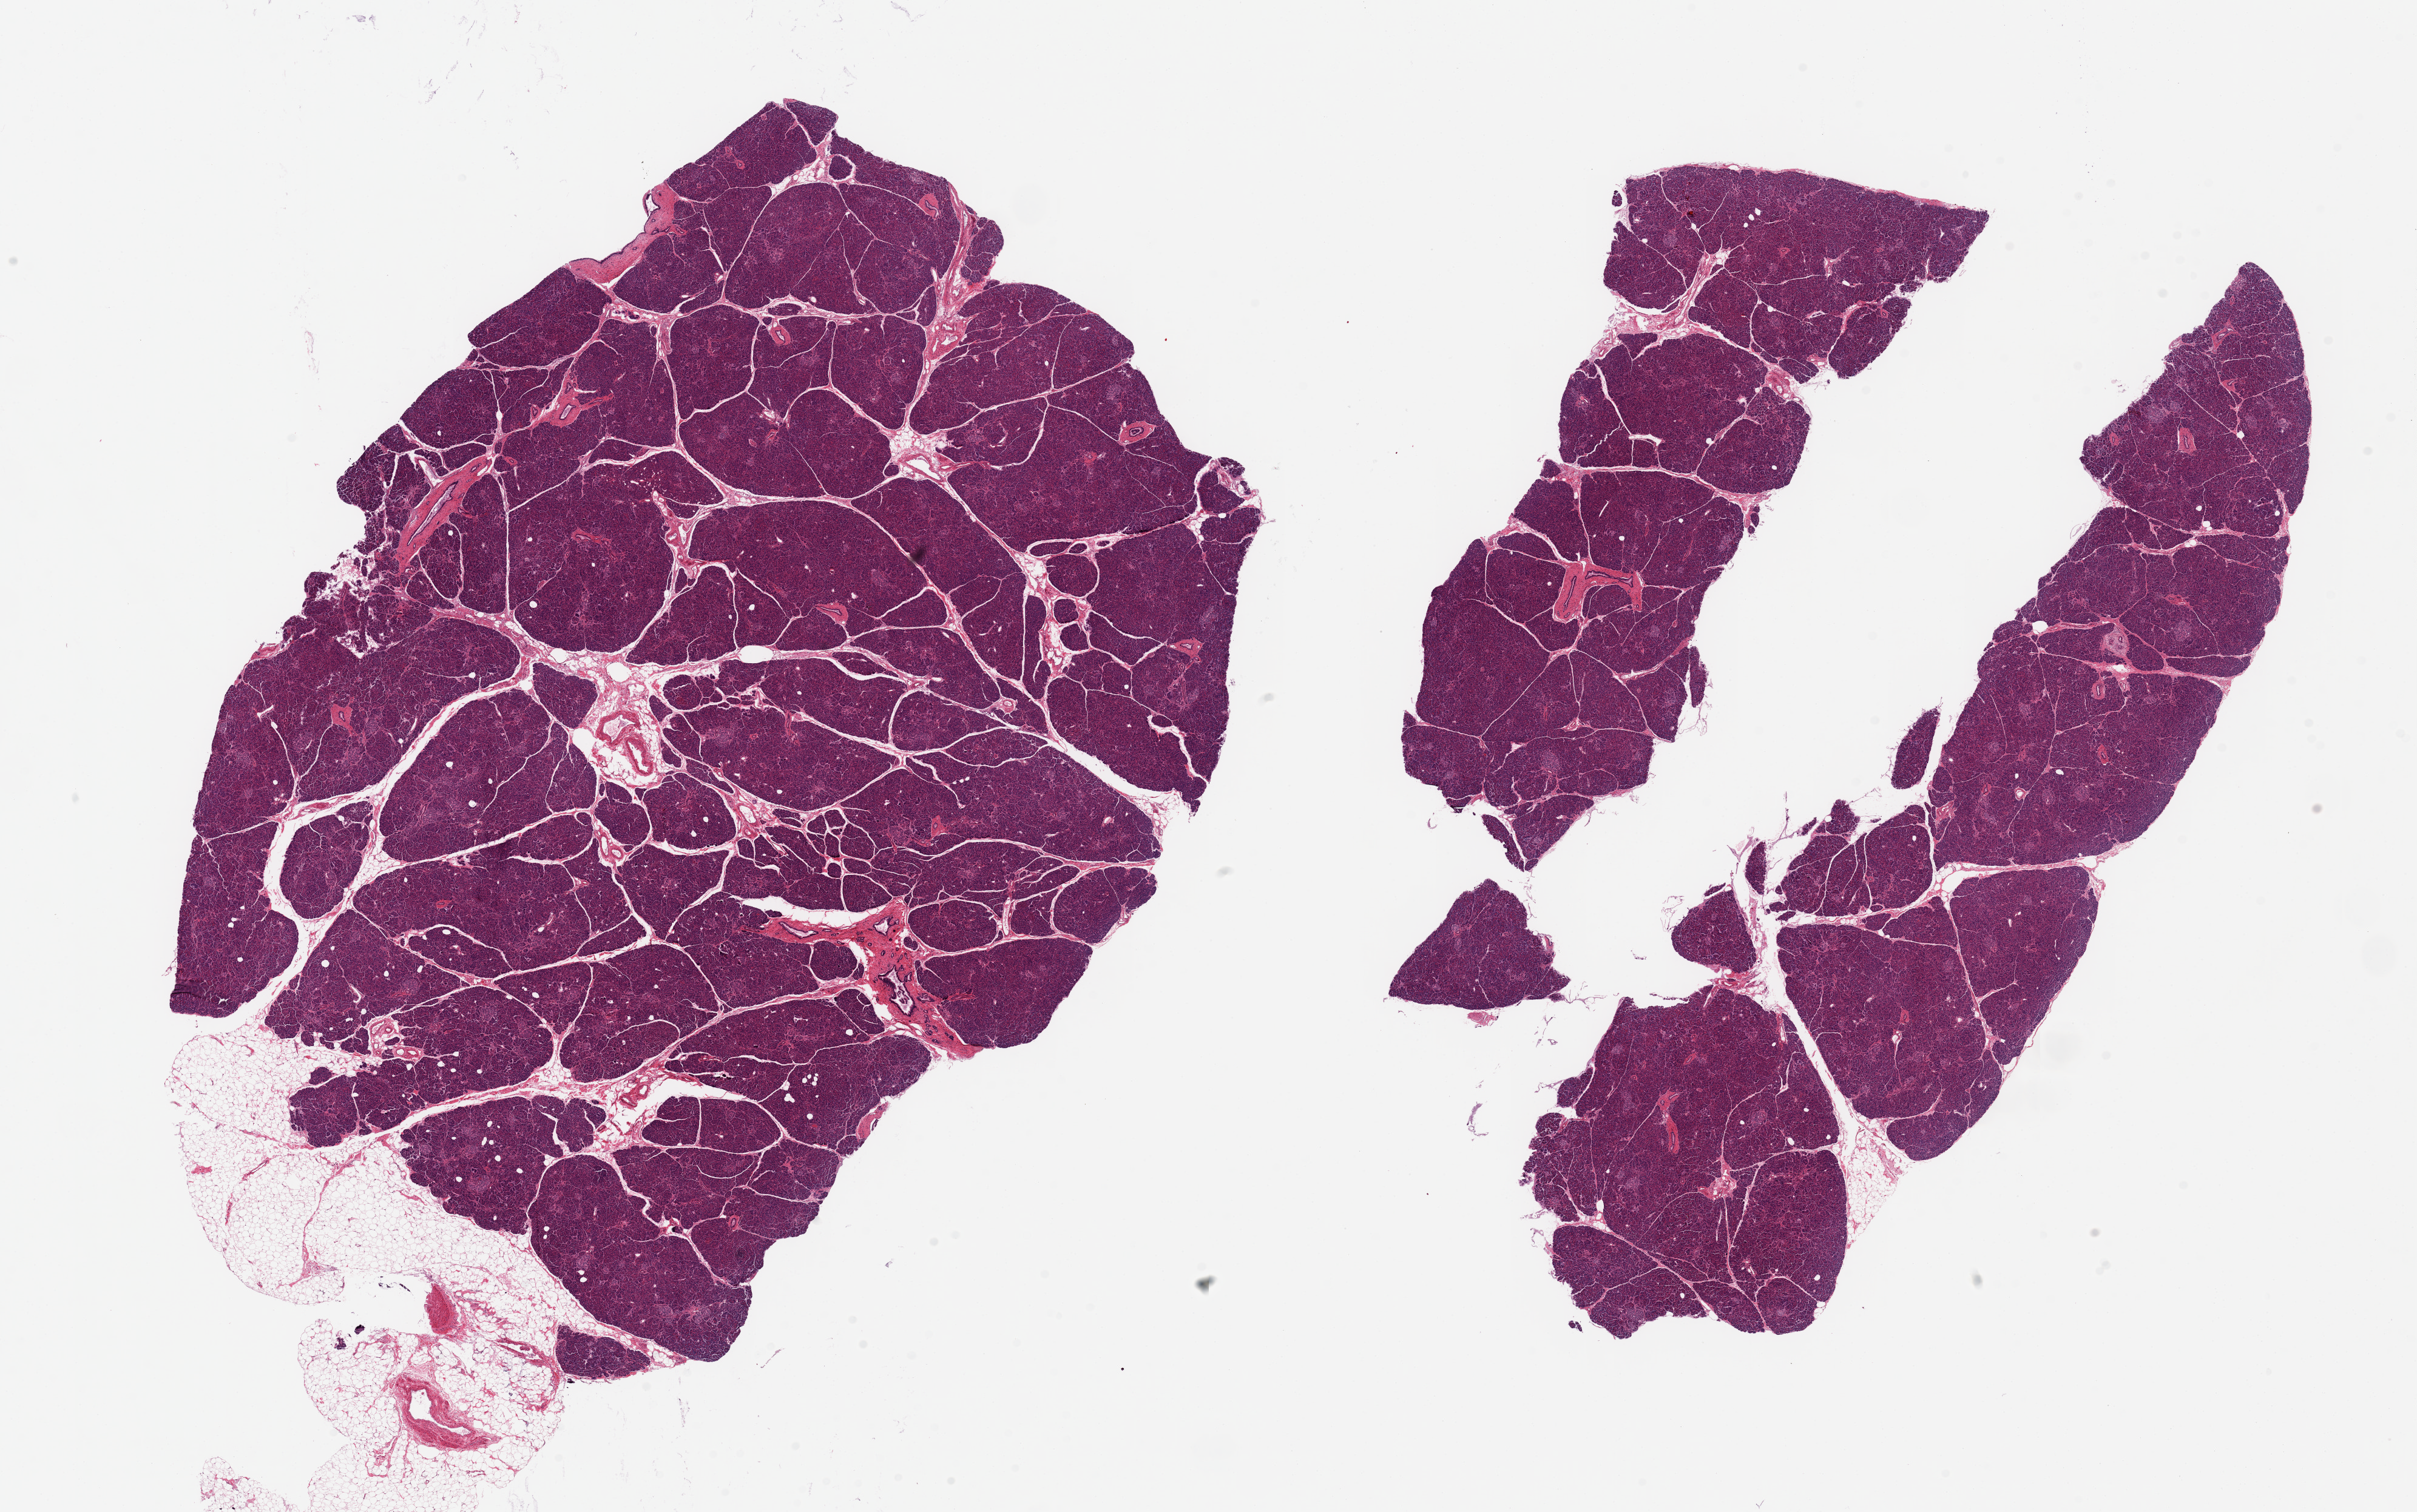
Digitized haematoxylin and eosin-stained section — low-resolution overview of the scanned area, about 31.5 x 19.7 mm (from a 20x scan); PAXgene-fixed, paraffin-embedded tissue; section of pancreas (target tissue); donor tissue sample. Donor sex: male.
- pathologist's review note for this sample: 2 pieces, 20x12 & 16x9.5mm; extremely well preserved parenchma with minimal interstitial fat; Islets well-seen